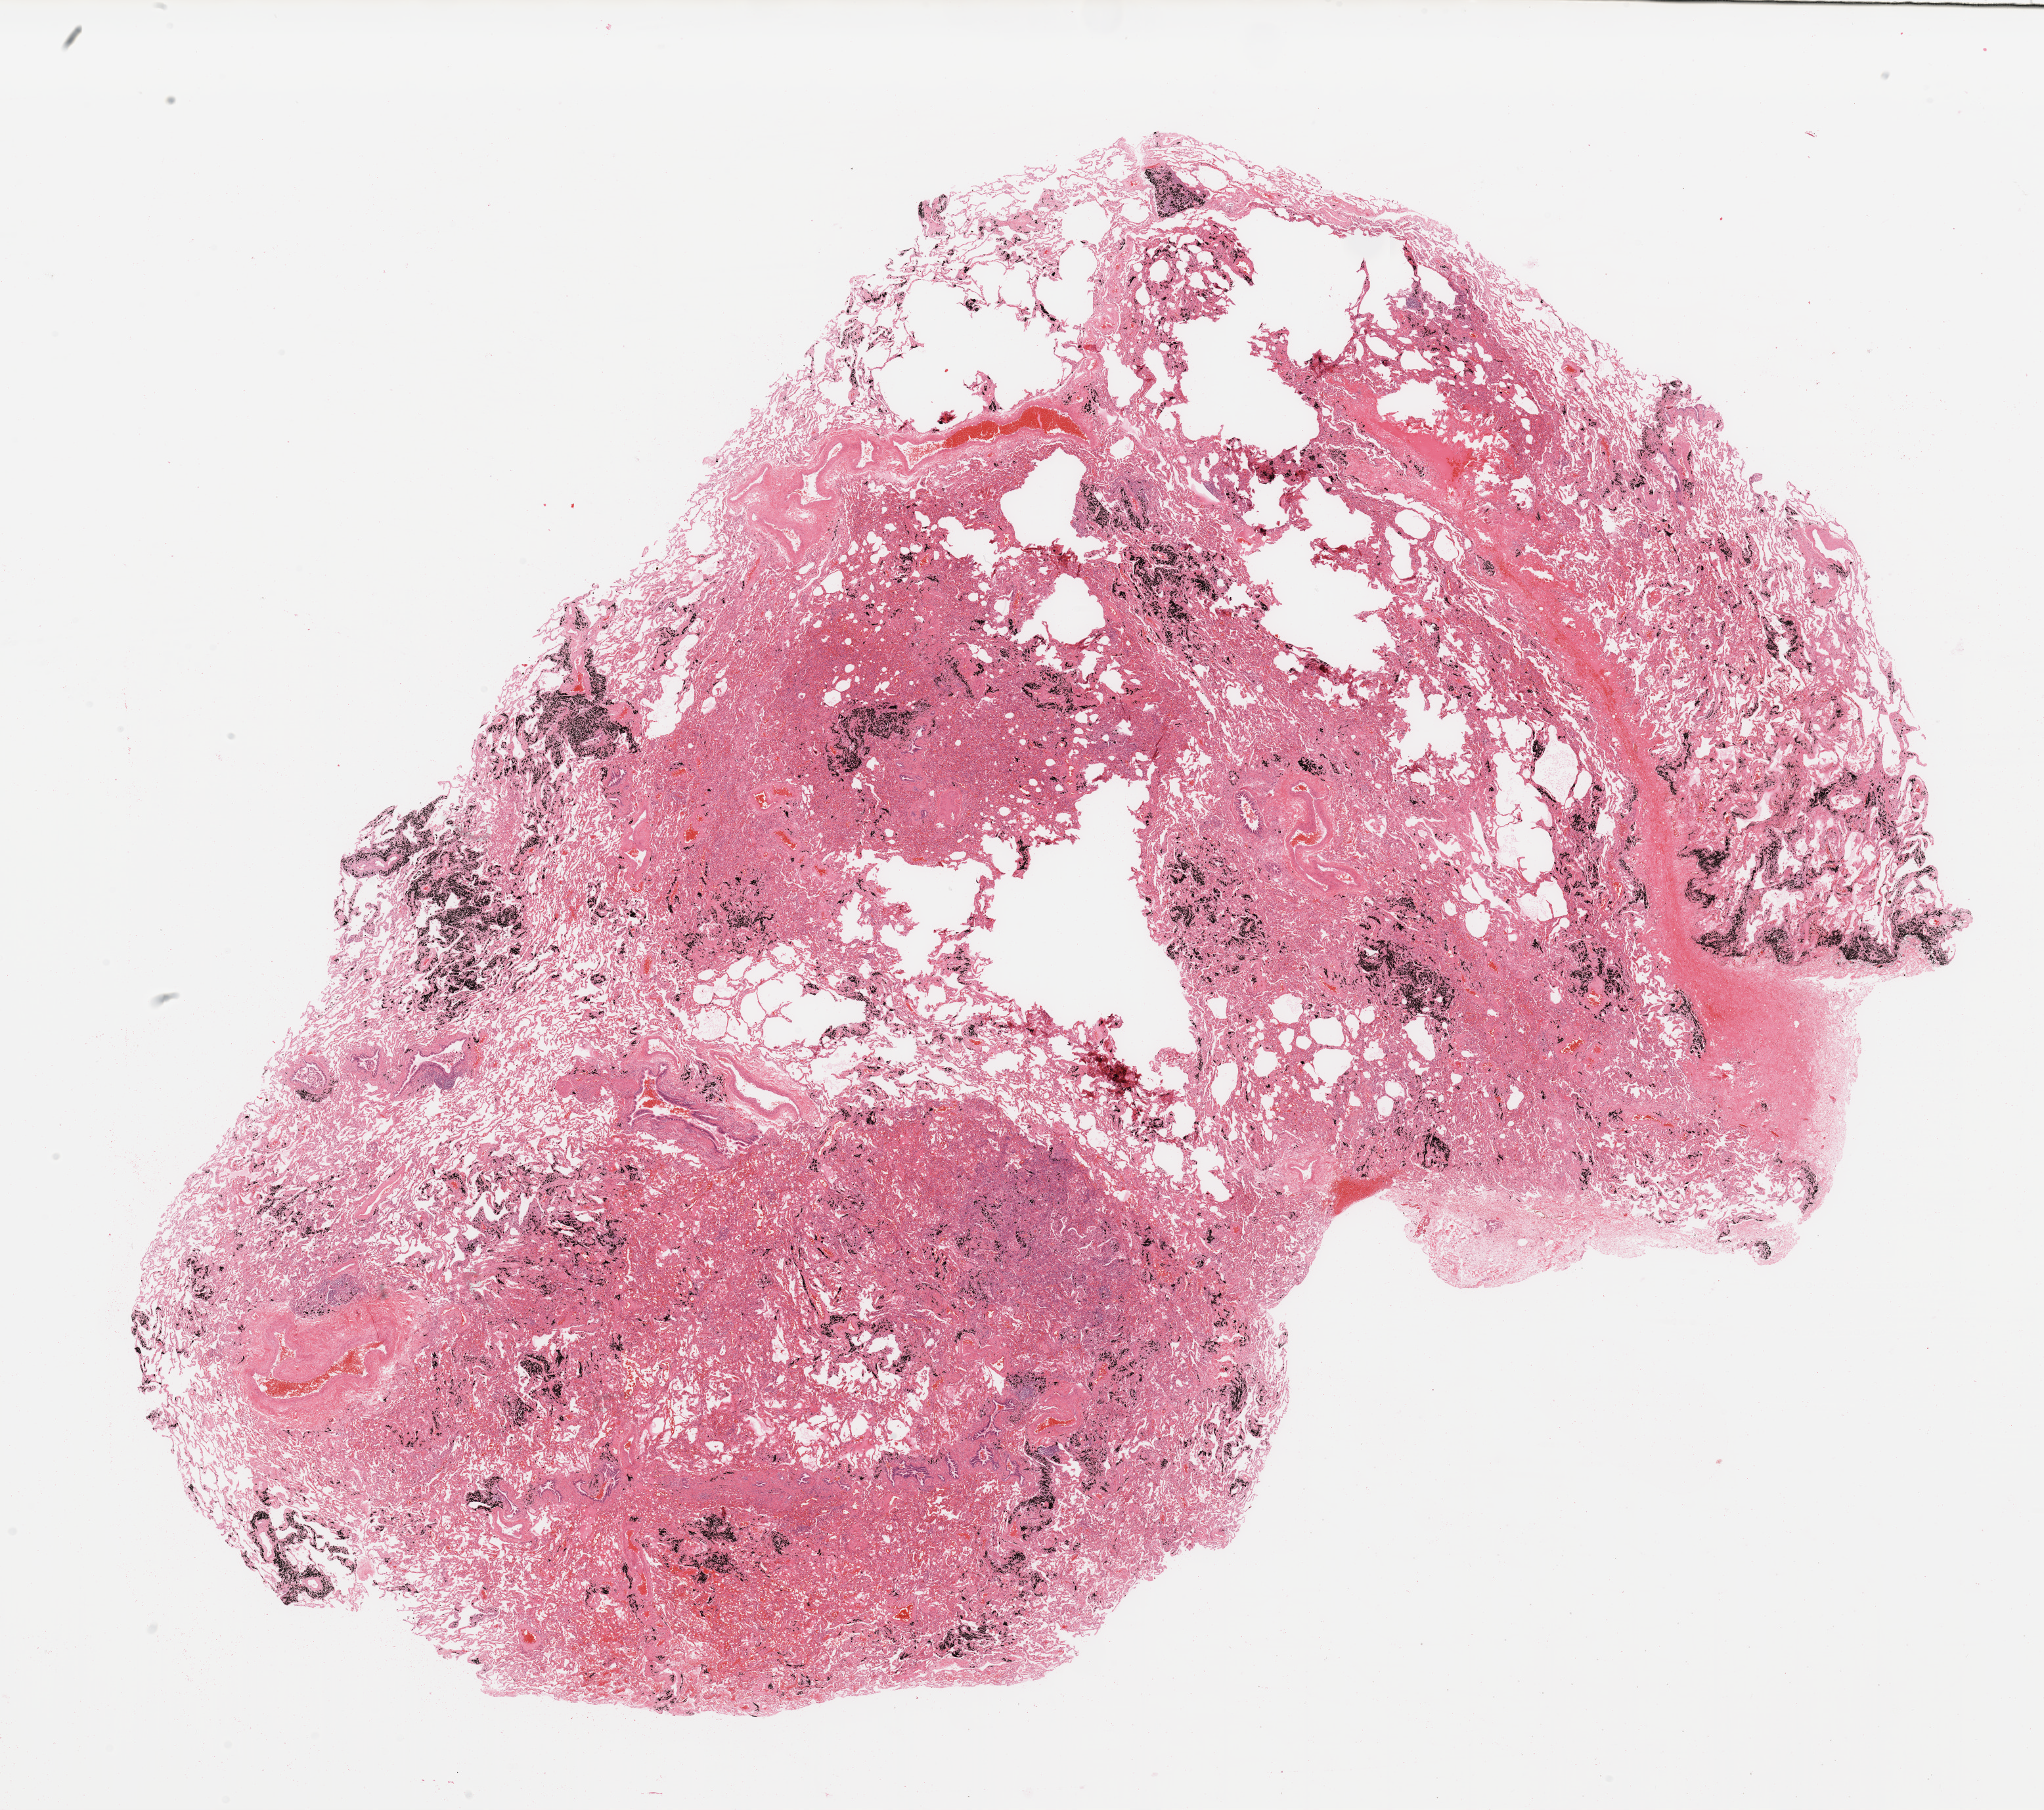
Hematoxylin and eosin (H&E) stained whole-slide image — a low-resolution overview of the entire scanned area, about 24.6 x 21.8 mm (slide scanned at 20x); normal (non-tumour) tissue sample, lung. Patient: male, age 65 years.
• this section: normal (non-tumour) tissue from the same patient
• patient diagnosis: Adenocarcinoma, NOS